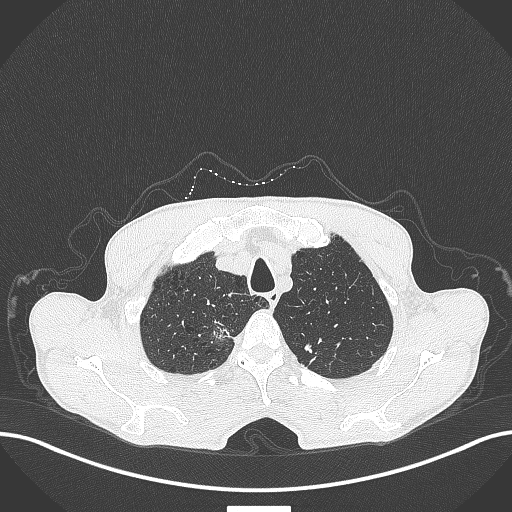
Chest CT, one axial slice. Slice 370 of 445 in the series (ordered by position). Reconstruction kernel B70f. 120 kVp. Lung window (W 1500 / L -600 HU). 1 mm slice thickness. 512 × 512 image matrix. Male patient, age 70 years. From the clinical record (not read from this slice): clinical TNM (as recorded): T1a N0 M0; histopathological grade: G1-2.
Outlined on this slice (bounding box drawn by a radiologist):
- lung tumour (recorded histology: adenocarcinoma): bounding box [x1, y1, x2, y2] px = [210, 319, 239, 346]